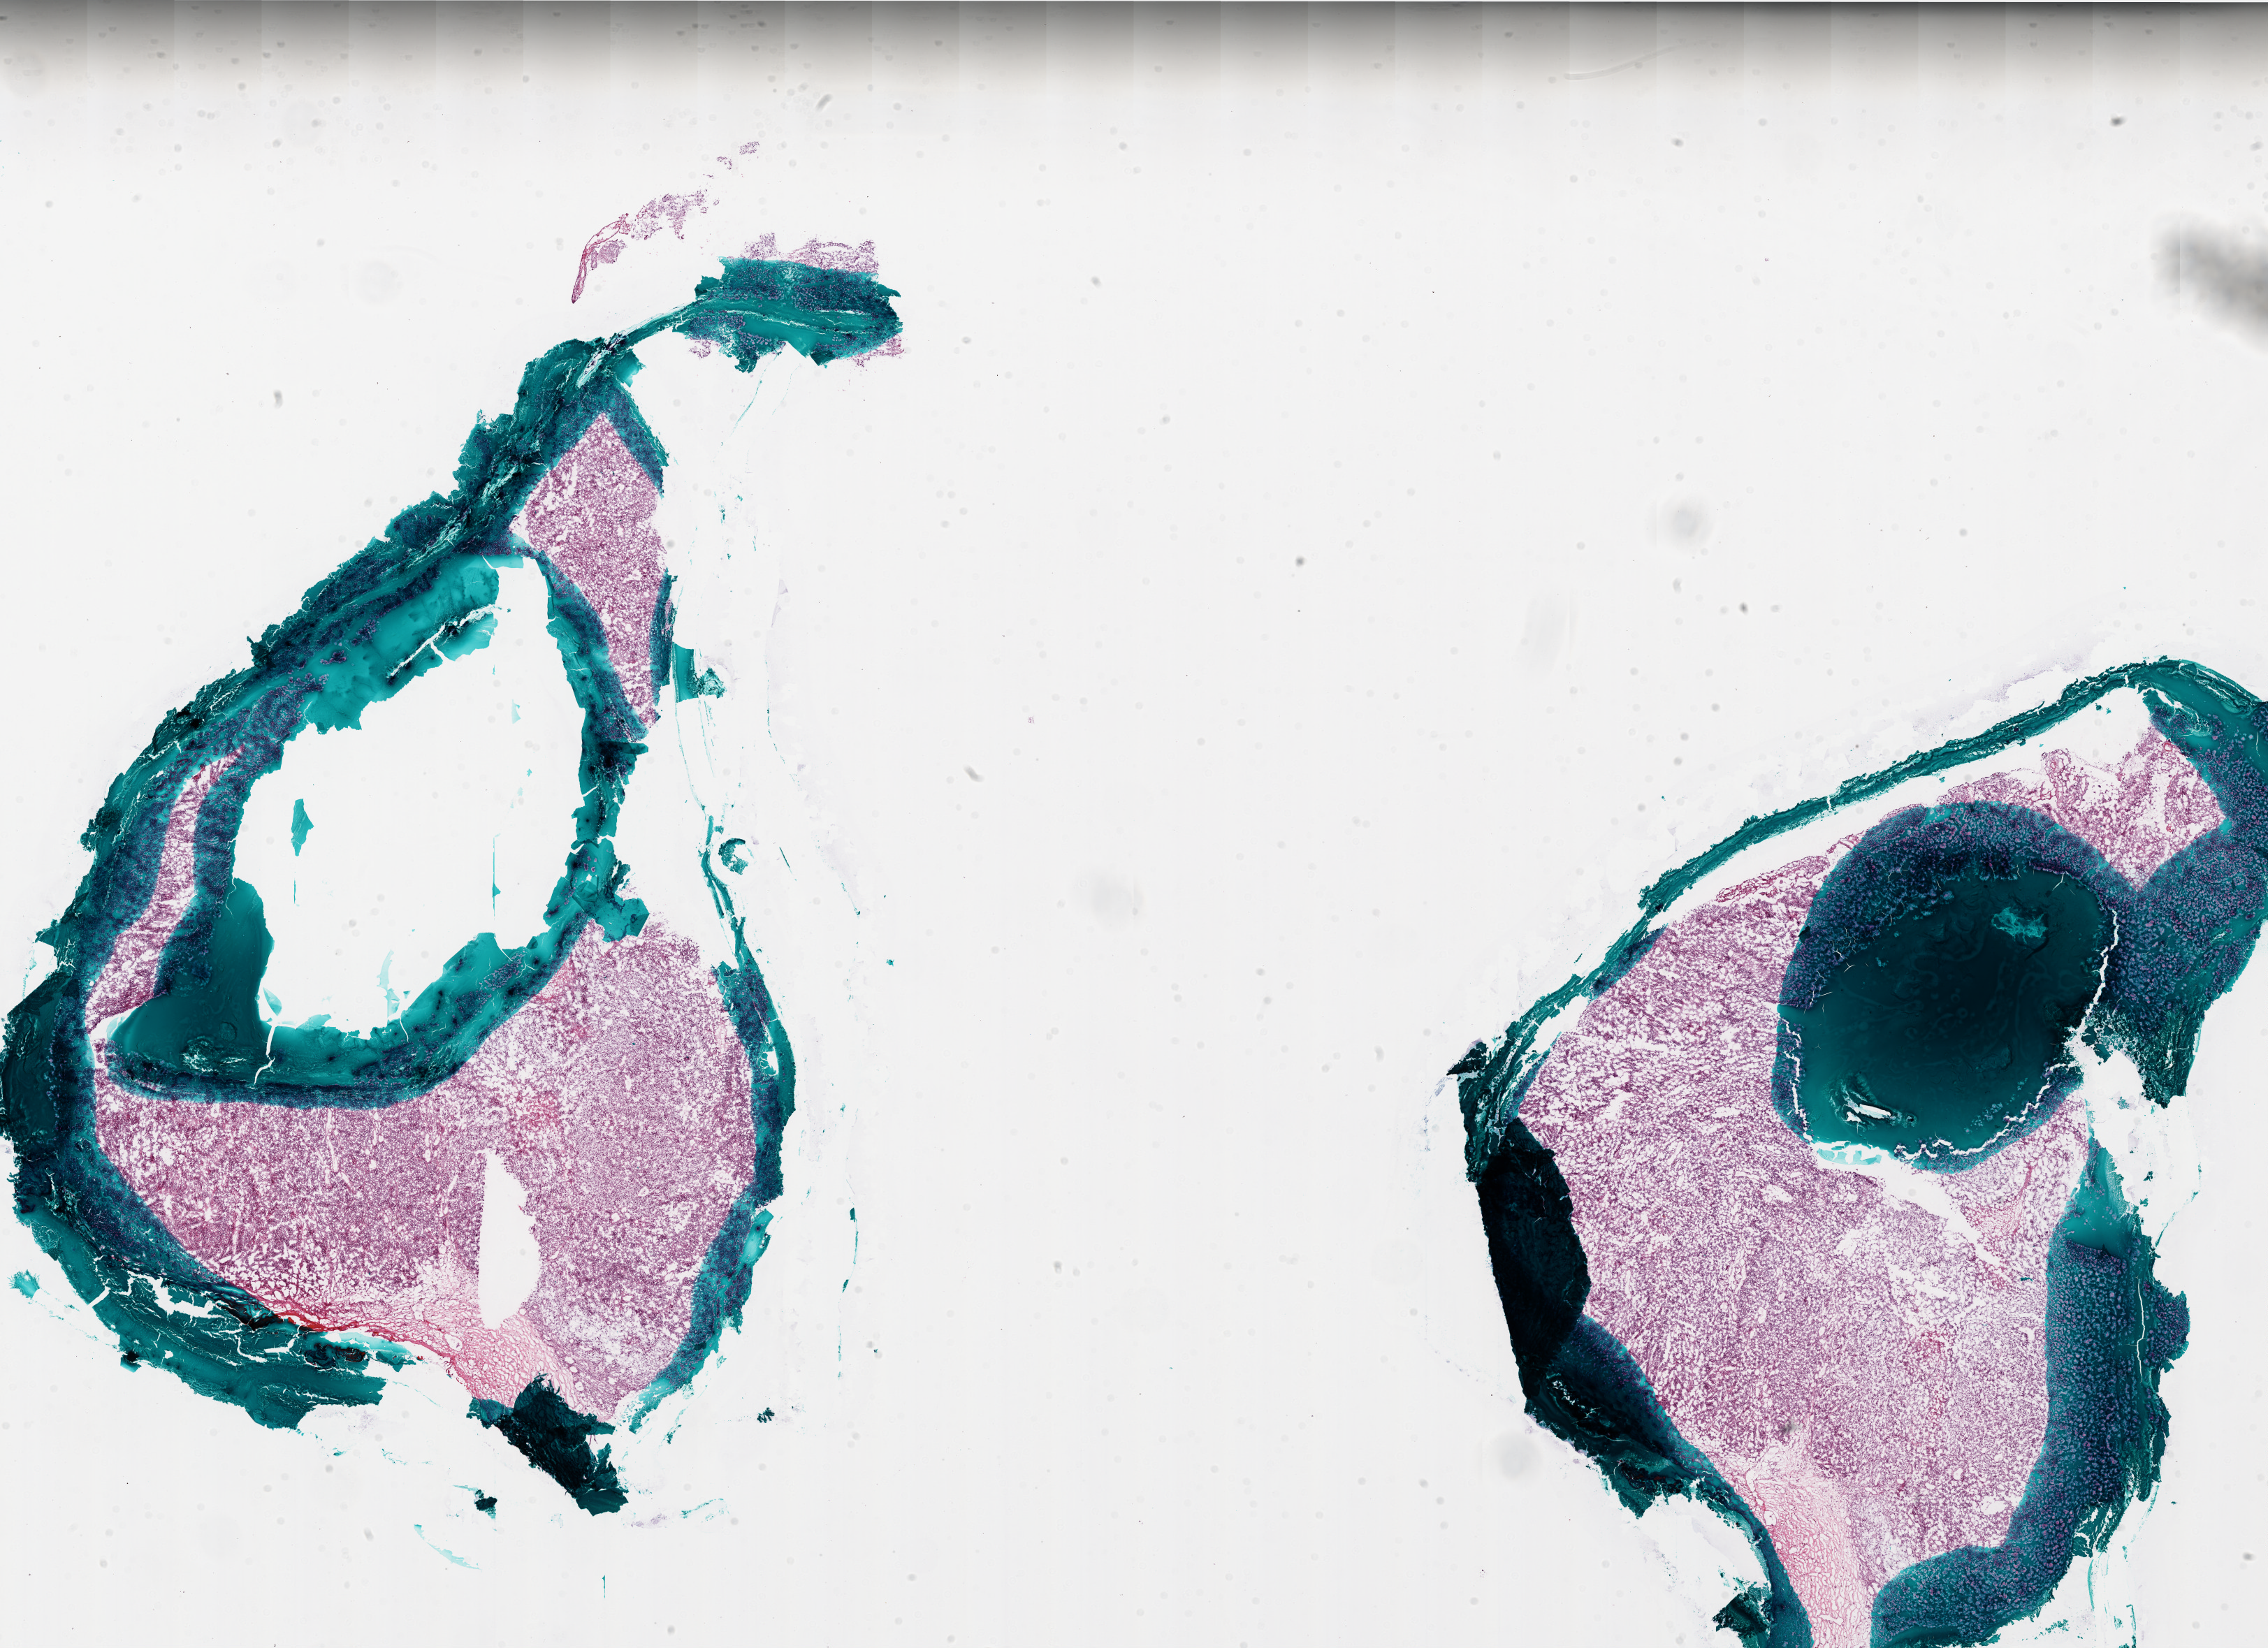
Digitized H&E tissue section (whole slide) — a low-resolution overview of the entire scanned area, about 26.0 x 18.9 mm; frozen section from the bottom of the tissue portion; brain, primary tumour sample. Male patient; age at initial diagnosis 54 years. Slide review estimates, as recorded: tumour cells 95%, tumour nuclei 100%, normal cells 0%, stromal cells 0%, necrosis 5%.
• histologic diagnosis: Glioblastoma